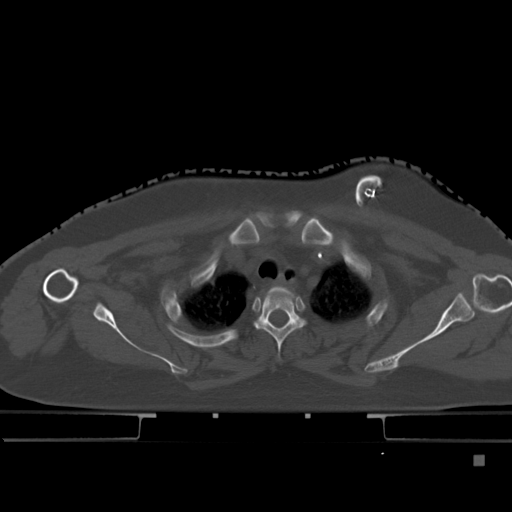
CT including the spine, one axial slice; slice 359 of 495 in the series (ordered by position); bone window (W 1800 / L 400 HU); 1.5 mm slice thickness; 512 × 512 image matrix, field of view 404 × 404 mm. Patient: female, 33 years. From the clinical record (not read from this slice): primary cancer: breast; vertebrae with lytic lesions (as recorded): T1.
Structures marked on this image (semi-automatic segmentation, software-assisted and operator-edited):
- T1 vertebra: bounding box (x1, y1, x2, y2) in pixels: (265, 286, 292, 298)
- T2 vertebra: (255, 291, 305, 361)